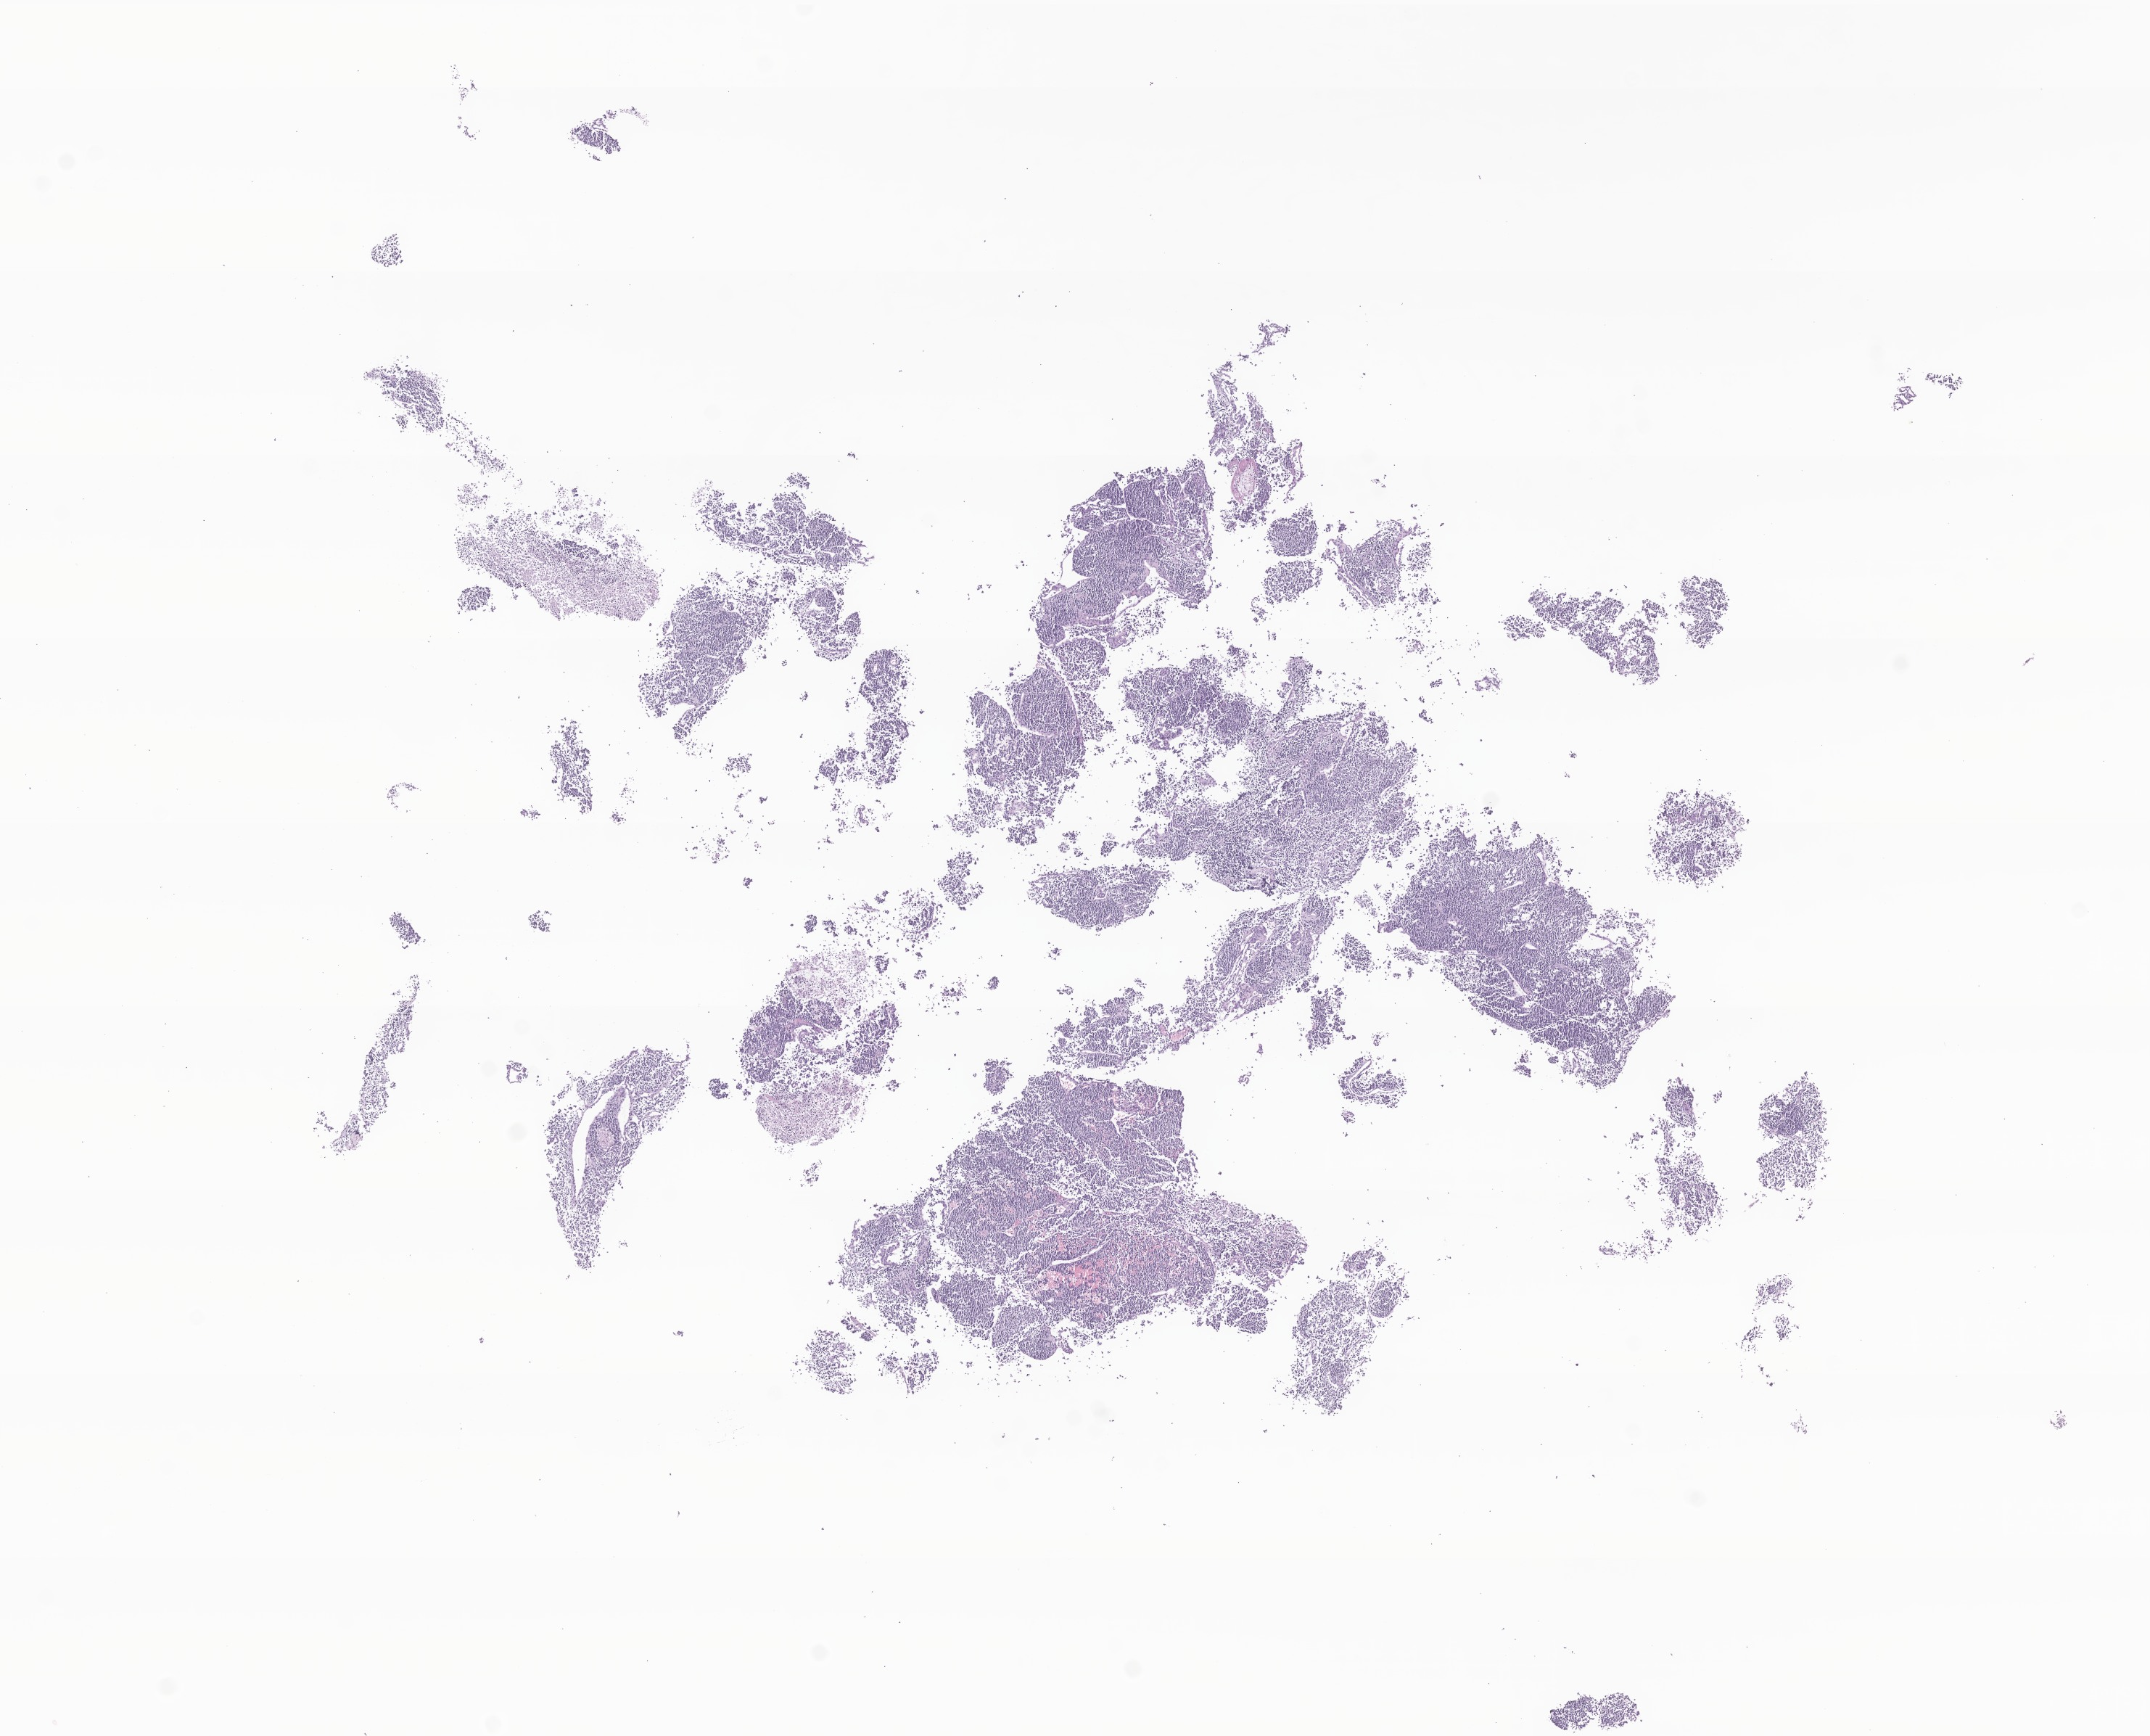
Whole-slide image, haematoxylin and eosin stain of tumor tissue from the vertebral column — a low-resolution overview of the entire scanned area, about 12.5 x 10.1 mm. Formalin-fixed, paraffin-embedded (FFPE) tissue. Patient: male, age 90 months (7 years 6 months).
Diagnosis (ICD-O-3 morphology term): Neuroblastoma, NOS.